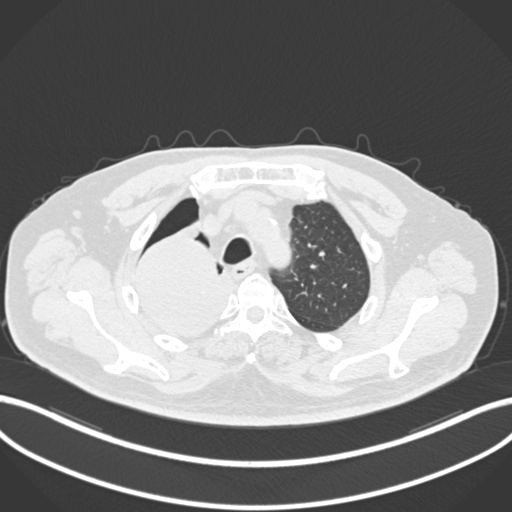
Chest CT, one axial slice; slice 171 of 218 in the series (ordered by position); lung window (W 1500 / L -600 HU); 1 mm slice thickness; 512 × 512 image matrix, field of view 400 × 400 mm. Male patient, age 68 years. From the clinical record (not read from this slice): clinical TNM (as recorded): T2a N0 M0.
Outlined on this slice (rectangle marked by the reading radiologist):
- lung tumour (recorded histology: adenocarcinoma): bounding box (x1, y1, x2, y2) in pixels: (134, 229, 236, 334)